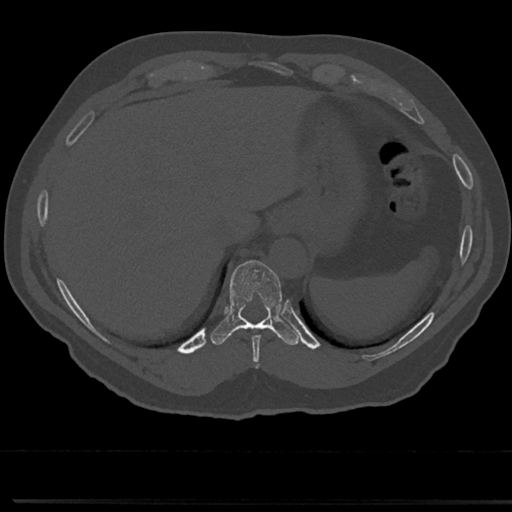
CT including the spine, one axial slice. Position 266 of 817 along the scan axis. Reconstruction kernel Br40s/3. 120 kVp. Bone window (W 1800 / L 400 HU). 0.5 mm slice thickness. 512 × 512 image matrix, field of view 355 × 355 mm. Patient: male, 61 years. Case-level facts recorded for this patient, not image findings: primary cancer: prostate.
Outlined on this slice (semi-automatically segmented with operator editing):
- T10 vertebra: box from (x=229, y=261) to (x=283, y=325) px
- T9 vertebra: (x=246, y=323)–(x=276, y=354)